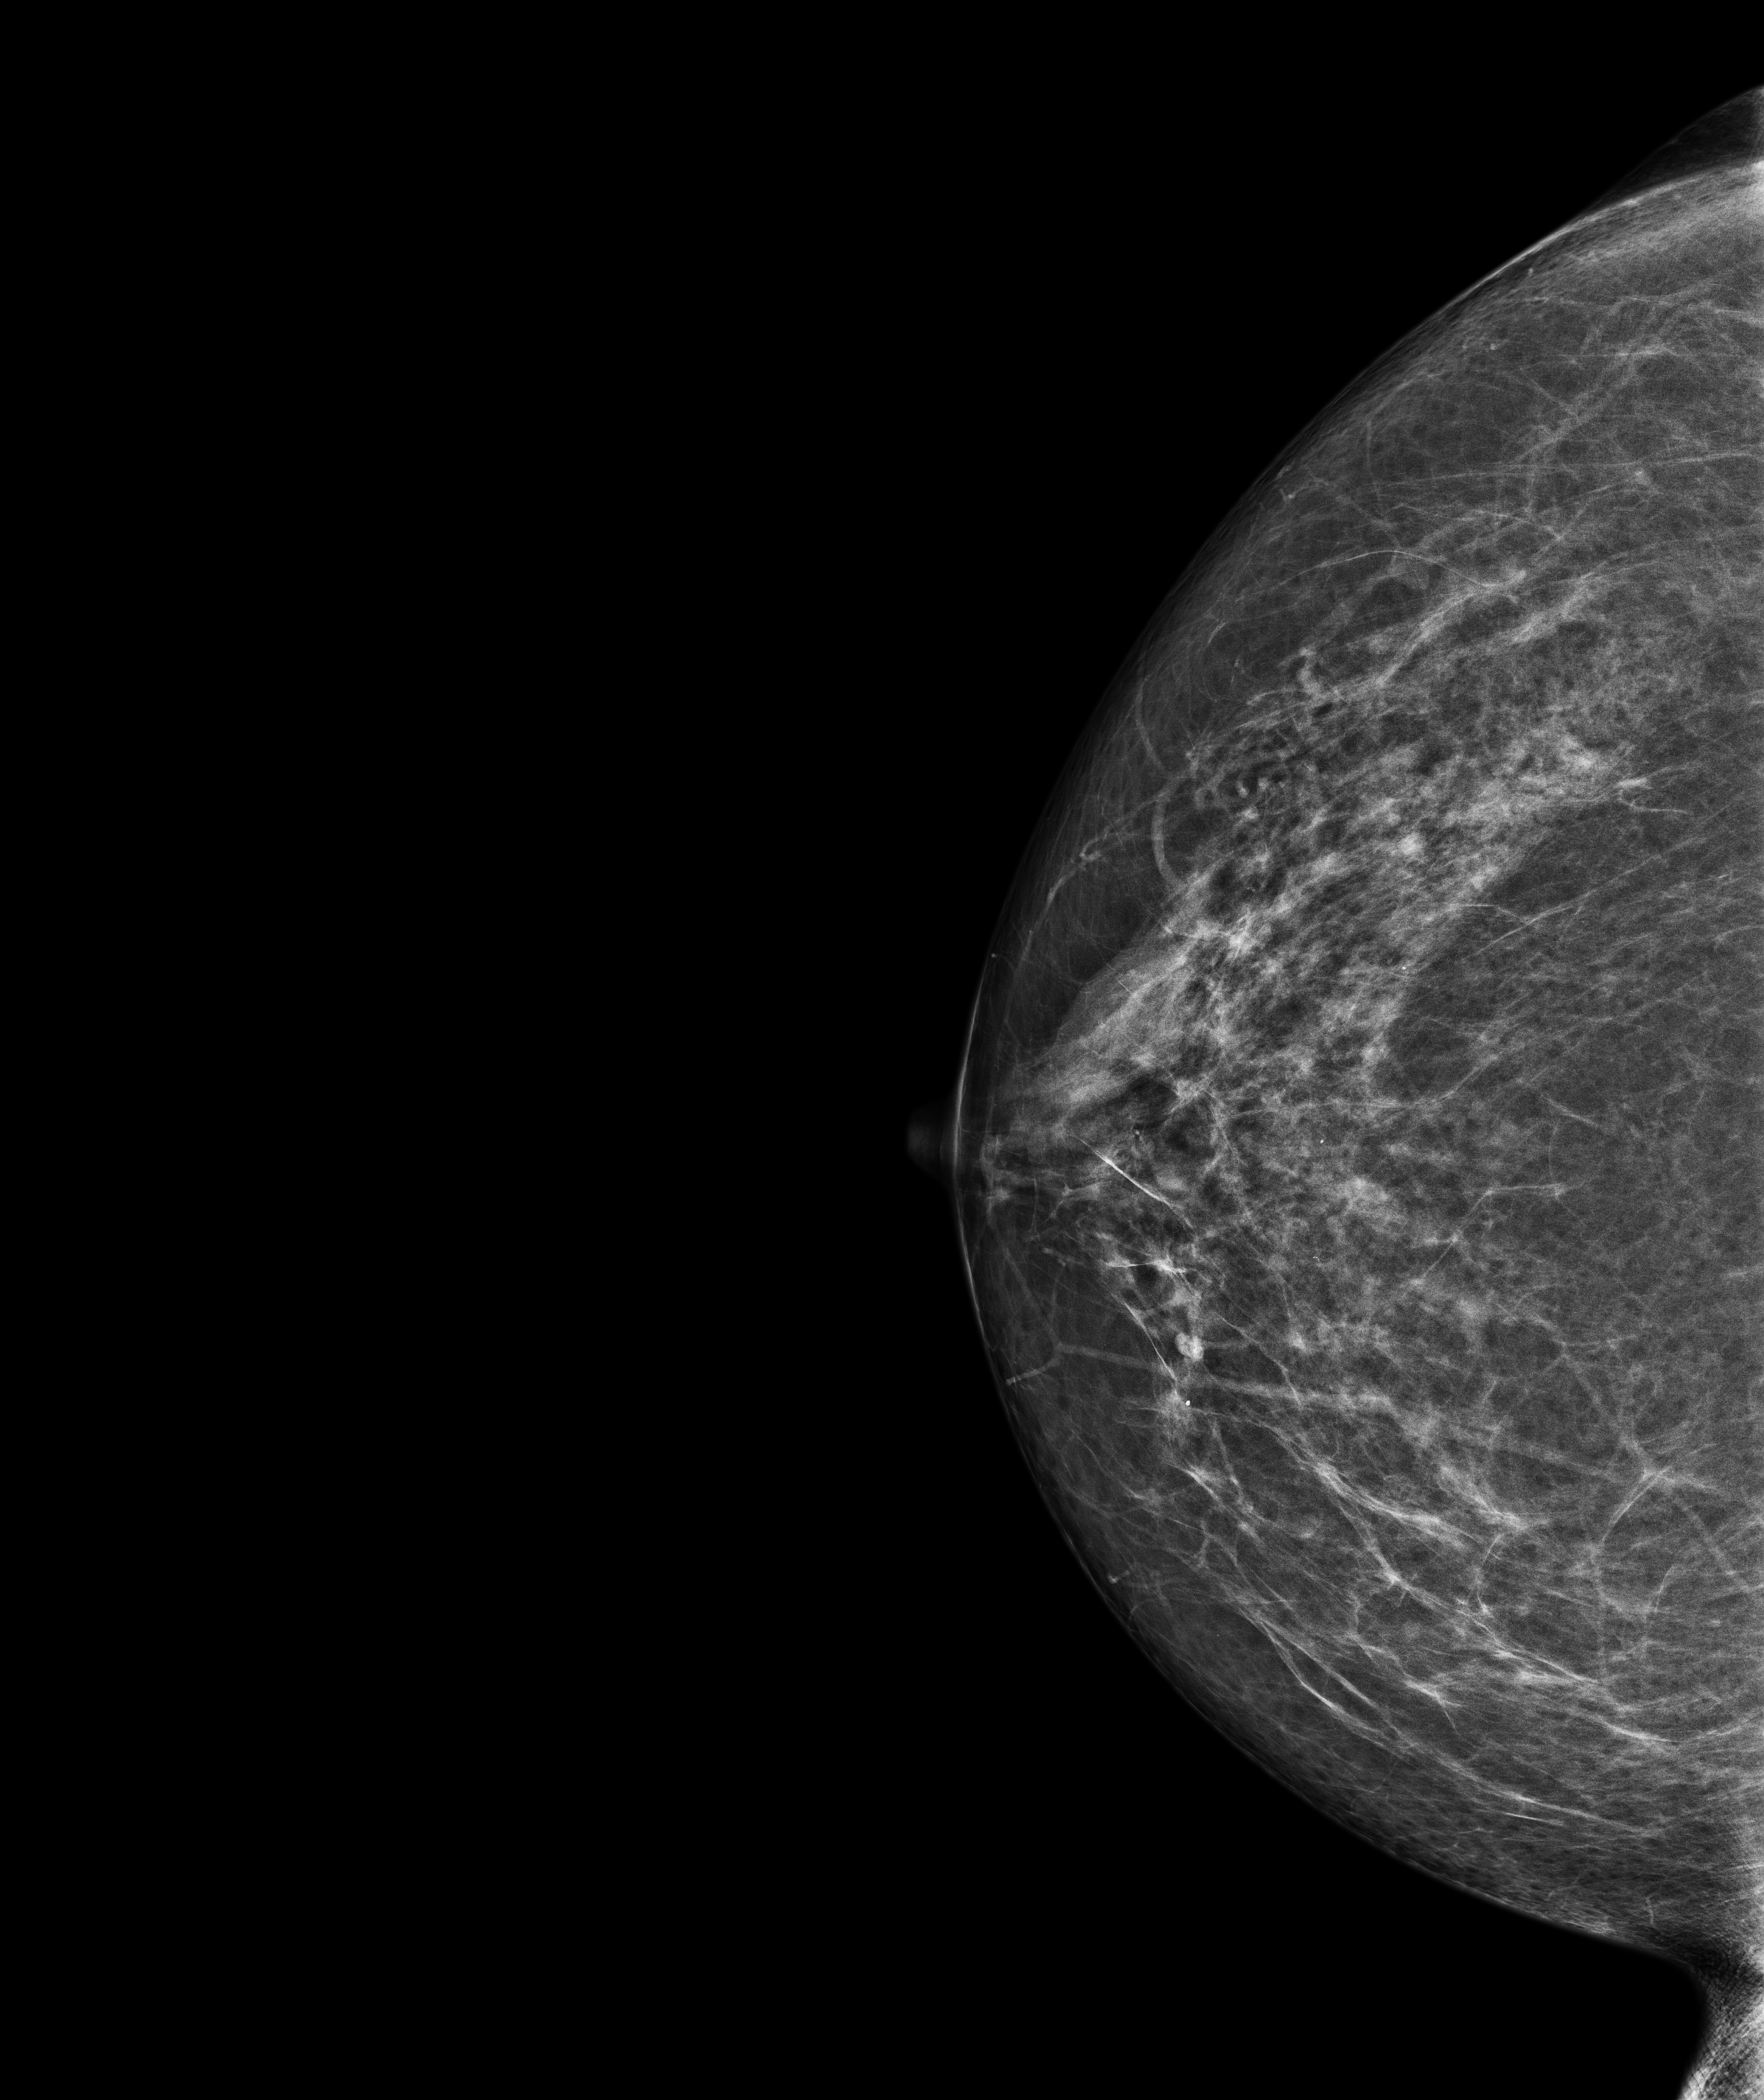
Annual screening mammography examination, compressed breast thickness 76.3 mm, system: Senographe Pristina. Patient aged 54 years (female).
Image type: full-field digital mammogram. Breast: right. Projection: cranio-caudal projection.